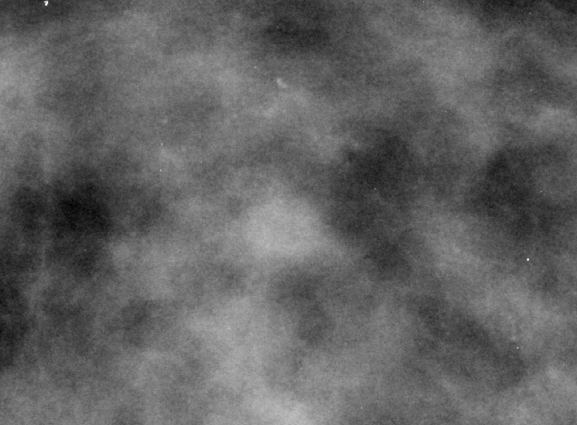
Region of interest cut from a scanned film mammogram (one marked finding), right breast, CC view.
Finding: calcifications, morphology pleomorphic, distribution clustered; BI-RADS assessment category 4; pathology result (as recorded, not read from the image): benign.